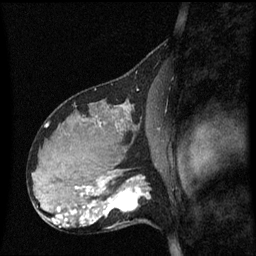
Breast MRI (dynamic contrast-enhanced), one sagittal slice. Position 34 of 60 along the scan axis. Dynamic contrast-enhanced series, image 2 of 3 at this slice position (ordered by acquisition). 1.5 T. TE 4.2 ms, TR 8.4 ms. 2.1 mm slice thickness. 256 × 256 image matrix, field of view 210 × 210 mm. Patient: female, 31 years. From the clinical record (not read from this slice): setting: breast cancer imaged before/during neoadjuvant chemotherapy; receptor status: HR-positive, HER2-negative.
Outlined on this slice (semi-automatic segmentation, software-assisted and operator-edited):
- analysis volume of interest (the breast-tissue region the enhancement analysis was run in; not a lesion): bounding box [x1, y1, x2, y2] px = [98, 175, 153, 228]
- tumour enhancement mask (voxels above the 70 % enhancement threshold inside the analysis volume of interest): [99, 177, 150, 216]